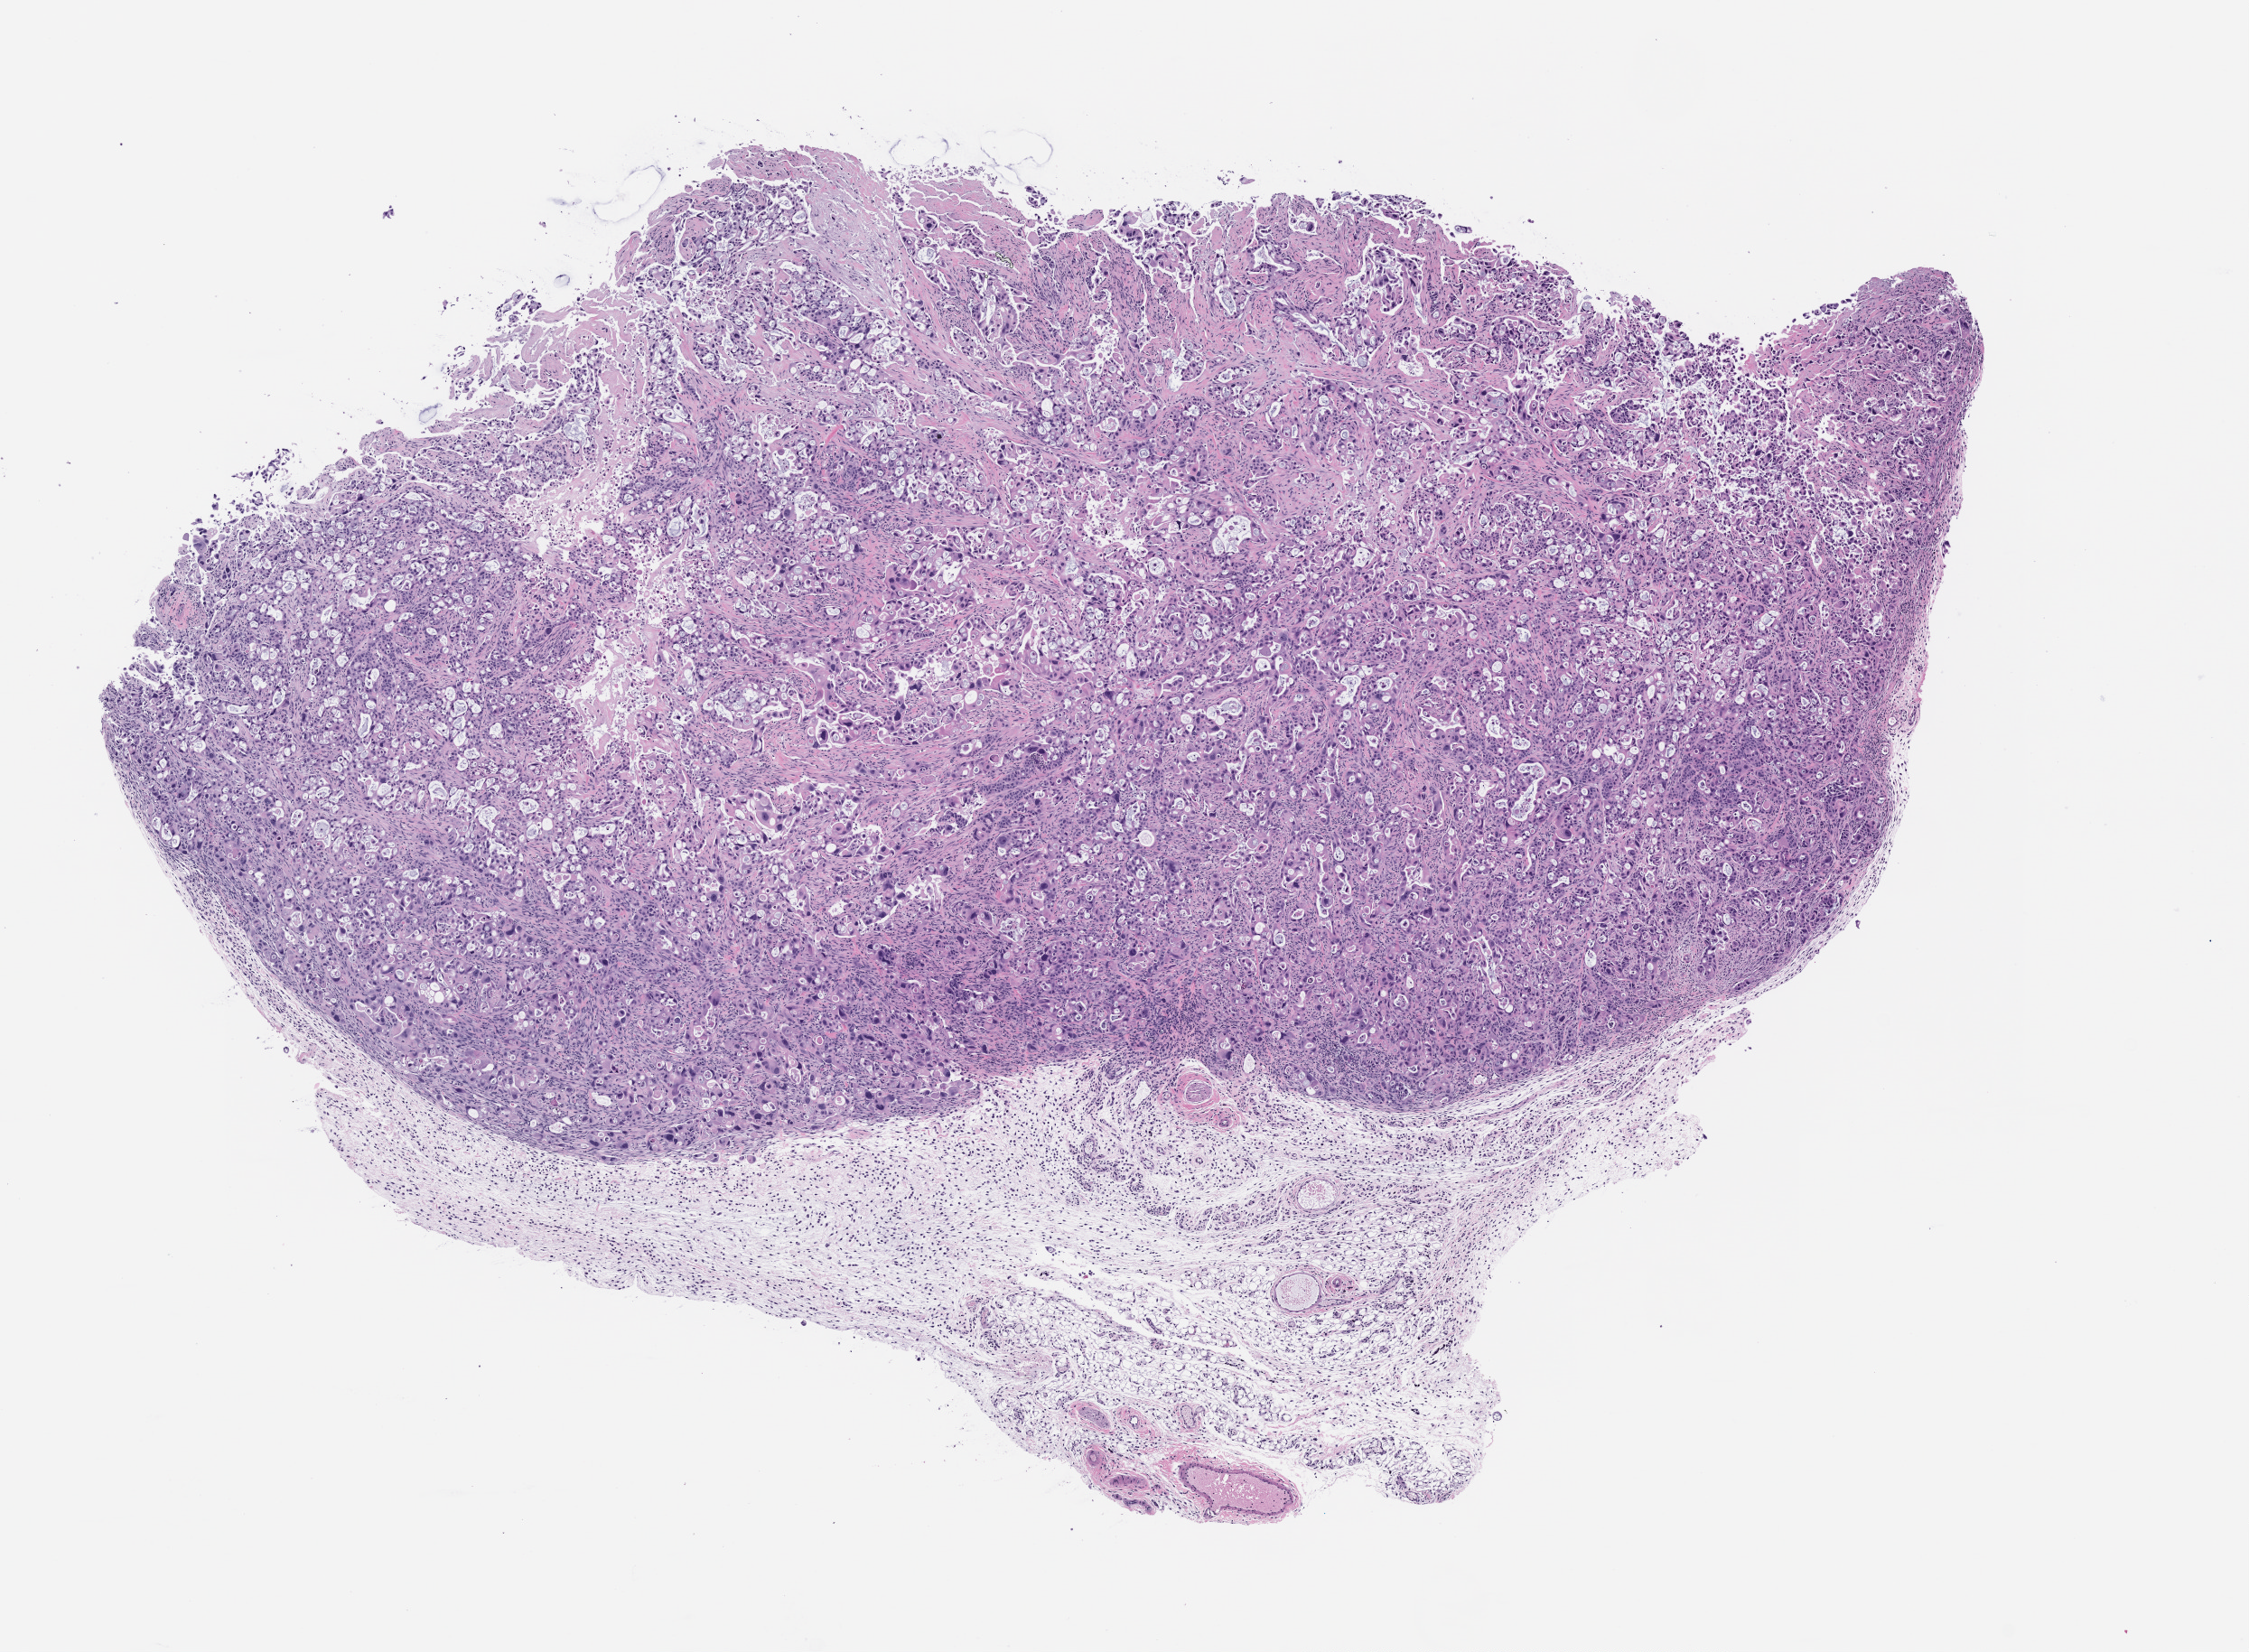
Whole-slide image, H&E: patient-derived xenograft (human tumor grown in a mouse), passage 0 — whole scanned area (about 10.0 x 7.4 mm) shown as a low-resolution overview; formalin-fixed, paraffin-embedded (FFPE) tissue; originating tumor site category: pancreas.
Originating patient diagnosis: Pancreatic Adenocarcinoma.